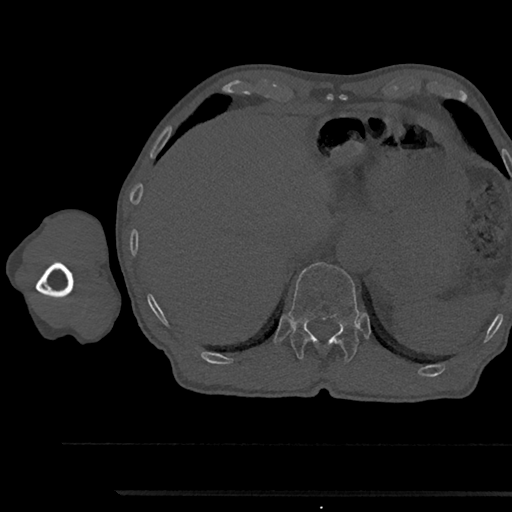
CT including the spine, one axial slice. Position 729 of 797 along the scan axis. 120 kVp. Bone window (W 1800 / L 400 HU). 512 × 512 image matrix, field of view 367 × 367 mm. Male patient, age 79 years. Case-level facts recorded for this patient, not image findings: primary cancer: prostate.
Structures marked on this image (semi-automatically segmented with operator editing):
- T12 vertebra: box from (x=288, y=262) to (x=359, y=362) px